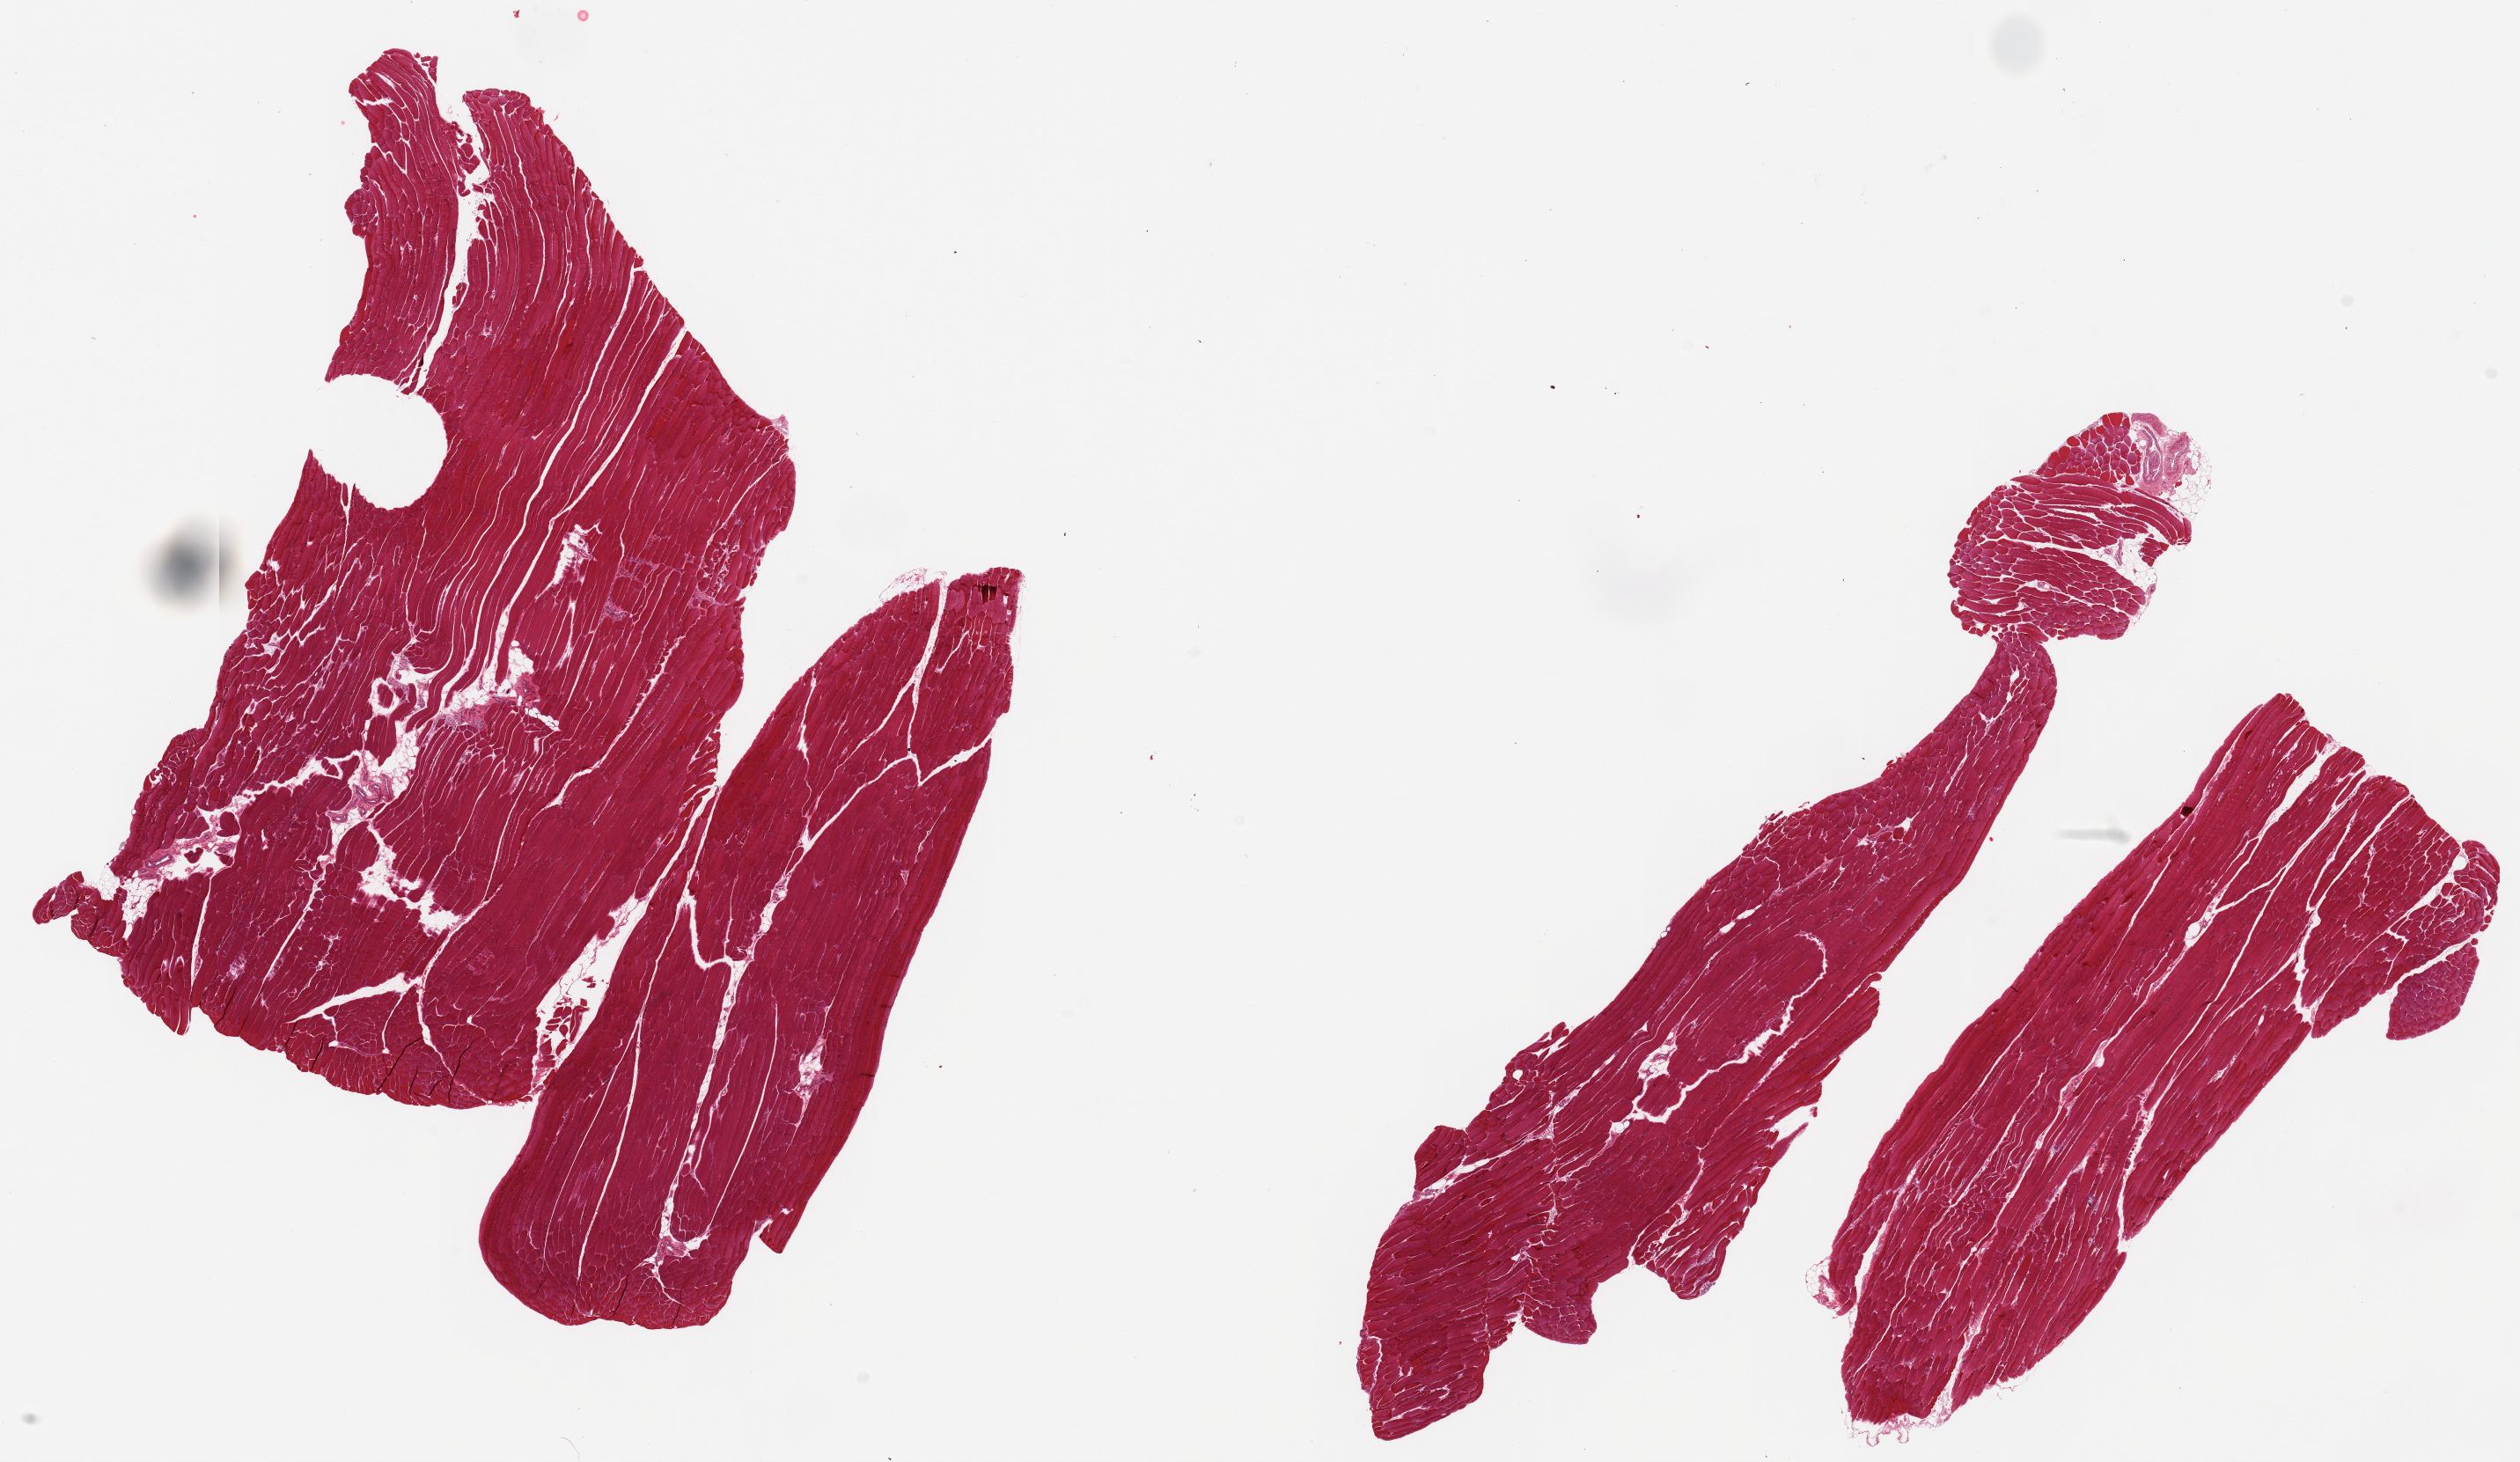
Whole-slide image, haematoxylin and eosin stain, low-resolution overview of the scanned area, about 22.6 x 13.1 mm (slide scanned at 20x), PAXgene-fixed paraffin-embedded (PFPE) section, section of skeletal muscle (target tissue), donor tissue sample.
* review note (as recorded): 2 pieces ~8x7mm, minimal interstitial fat